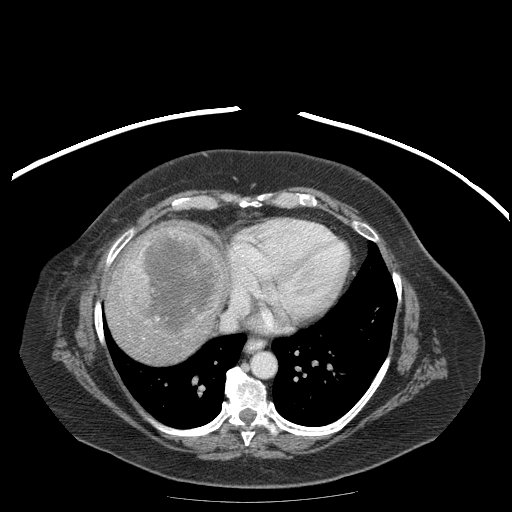
Contrast-enhanced abdominal CT (liver protocol), one axial slice; position 165 of 204 along the scan axis; reconstruction kernel STANDARD; soft-tissue window (W 400 / L 40 HU); 2.5 mm slice thickness; 512 × 512 image matrix. From the clinical record (not read from this slice): diagnosis: hepatocellular carcinoma (patient treated with transarterial chemoembolisation; whether this scan precedes or follows treatment is not stated here); TNM stage (as recorded): Stage-IIIB; Child-Pugh class: A; tumour differentiation: well differentiated; tumour nodularity: uninodular.
Outlined on this slice (semi-automatic segmentation, software-assisted and operator-edited):
- liver parenchyma outside the tumour (the mass and vessels are separate outlines, so this box may not span the whole liver): bounding box (x1, y1, x2, y2) in pixels: (104, 224, 226, 364)
- mass: (120, 230, 225, 338)